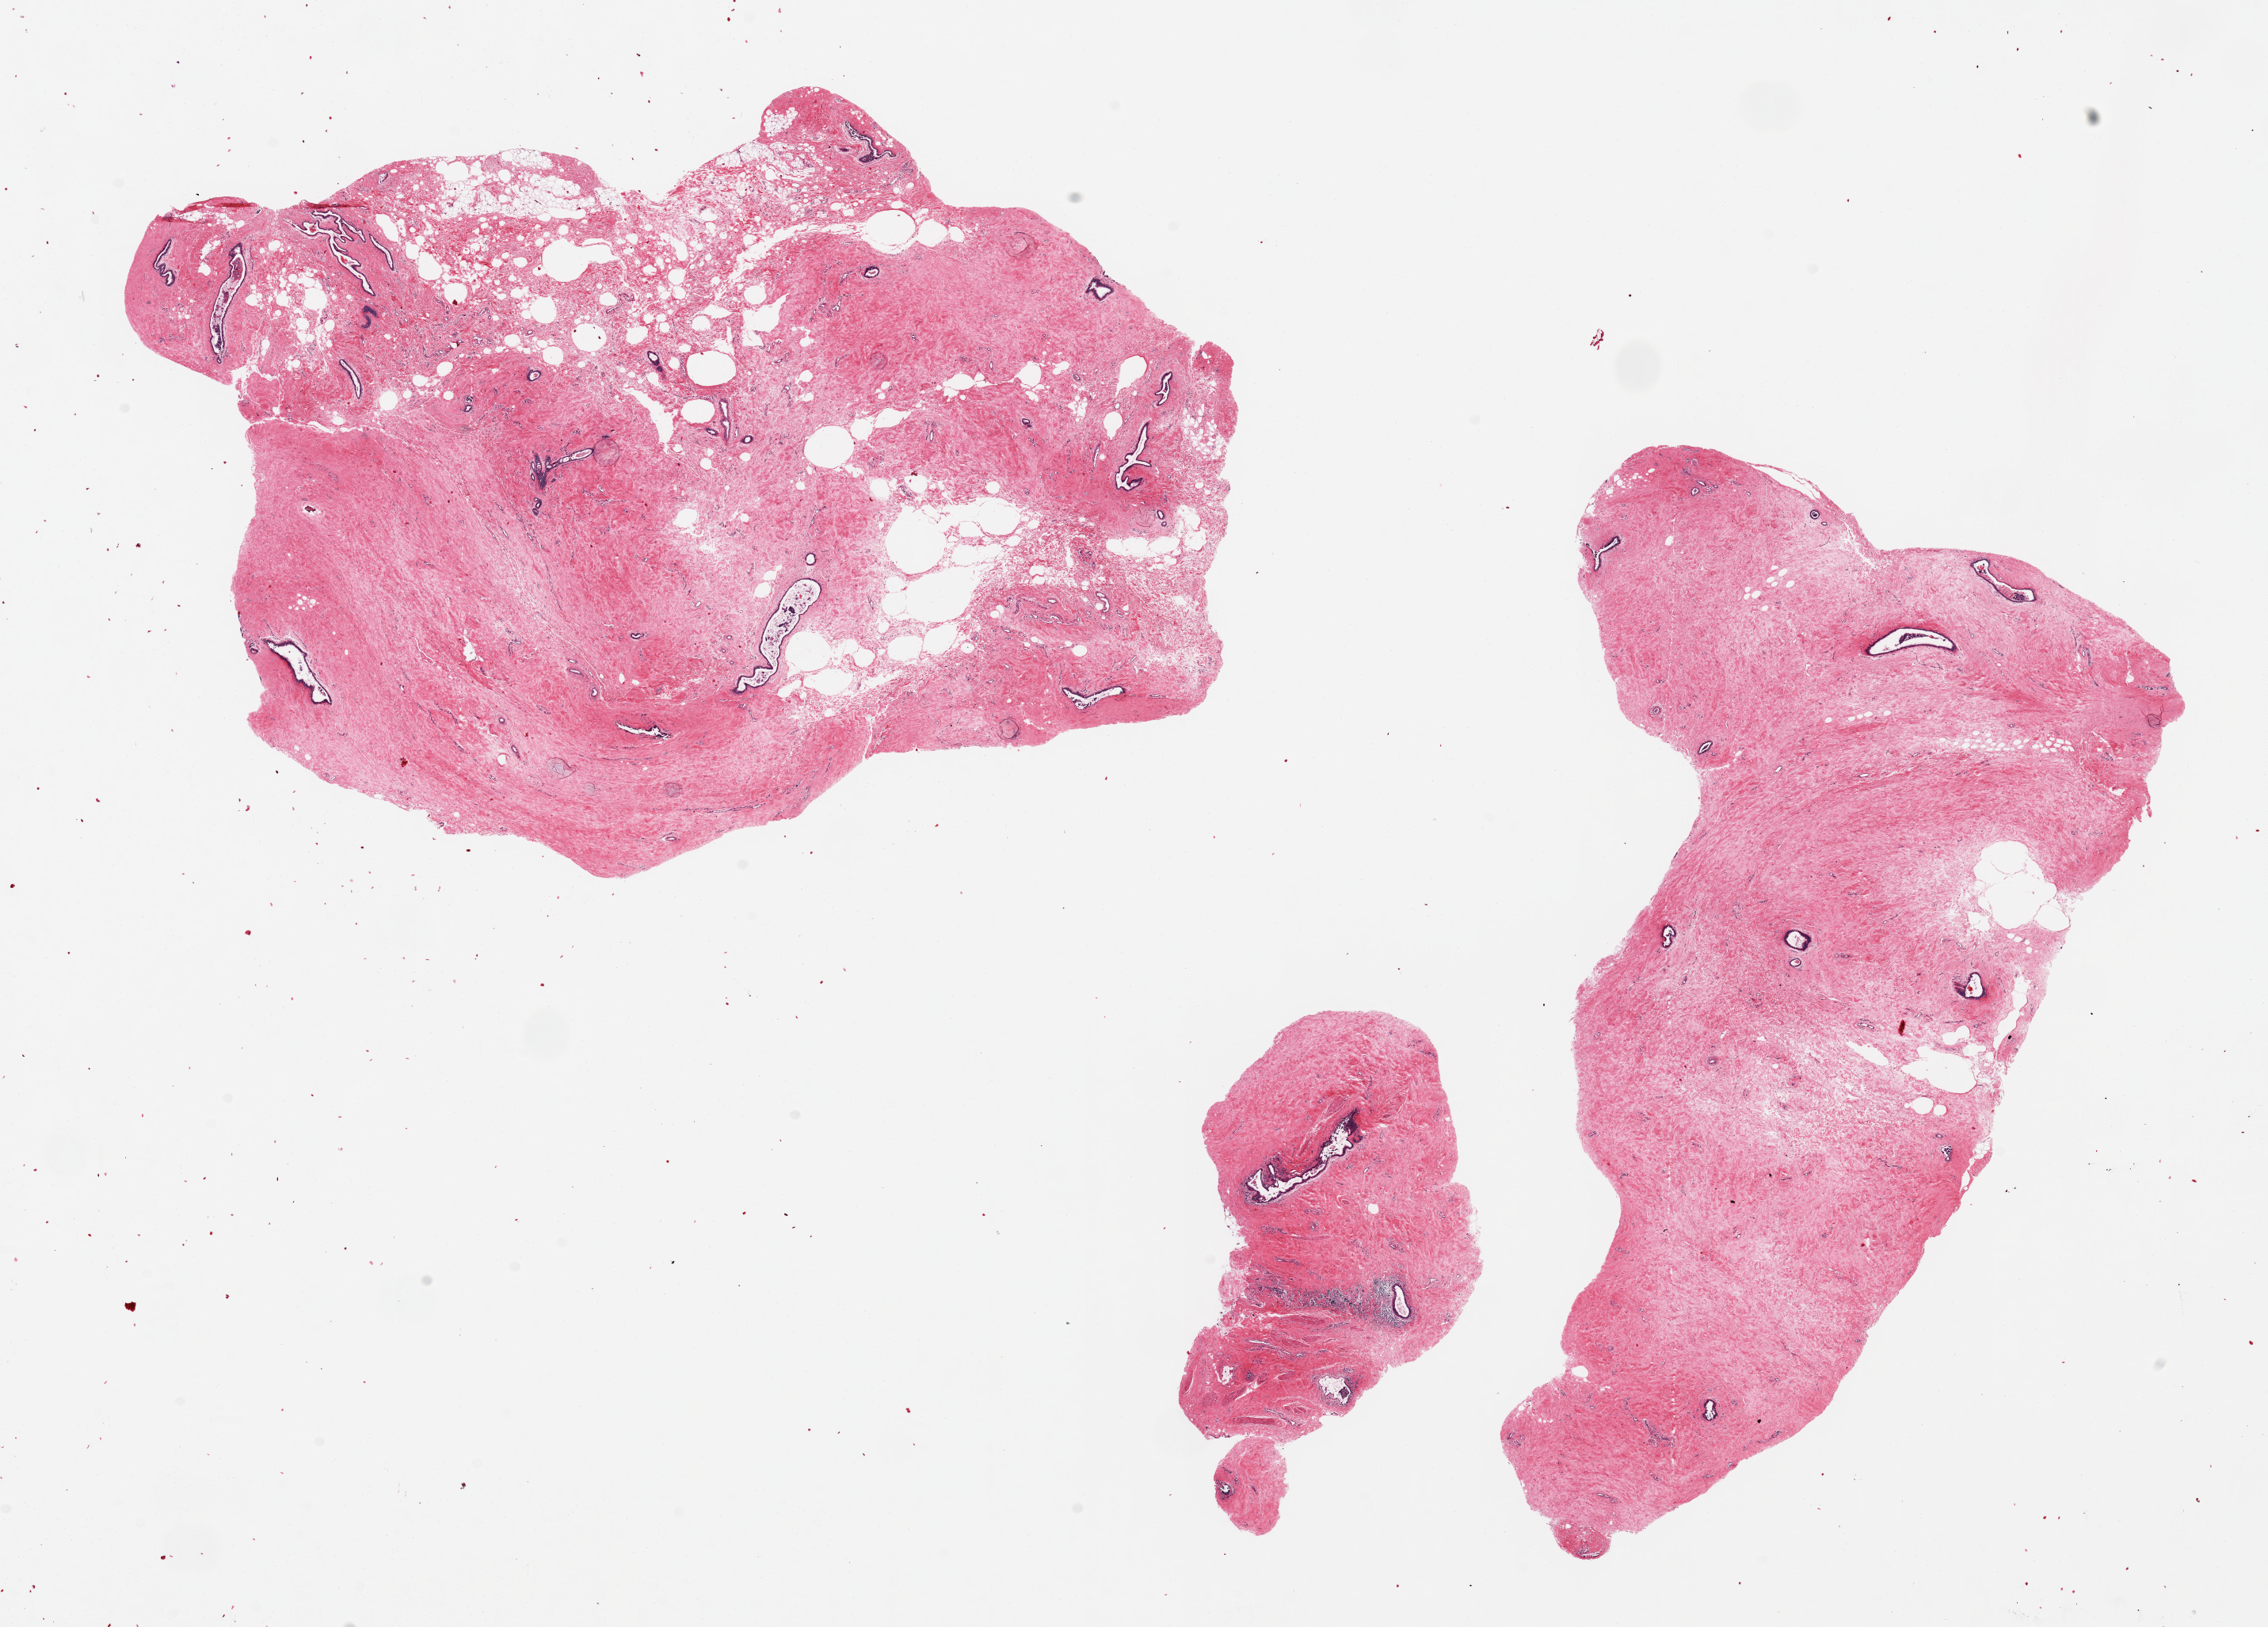
Digitized haematoxylin and eosin-stained section — low-resolution overview of the scanned area, about 22.6 x 16.2 mm (acquisition: 20x scan); PAXgene-fixed, paraffin-embedded tissue; target tissue: breast; donor tissue sample. Donor sex: male.
* review note (as recorded): 2 pieces ductal elements present